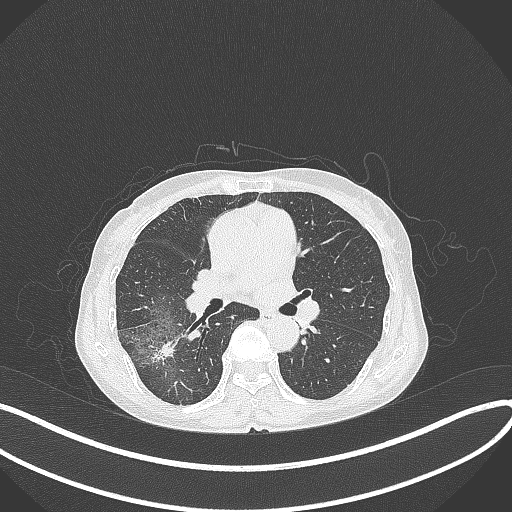
Chest CT, one axial slice. Position 217 of 371 along the scan axis. Reconstruction kernel B70f. 120 kVp. Lung window (W 1500 / L -600 HU). 512 × 512 image matrix, field of view 400 × 400 mm. Female patient, age 69 years. From the clinical record (not read from this slice): clinical TNM (as recorded): T1b N0 M0; histopathological grade: G2-3.
Outlined on this slice (rectangle marked by the reading radiologist):
- lung tumour (recorded histology: adenocarcinoma): box from (x=149, y=334) to (x=183, y=367) px